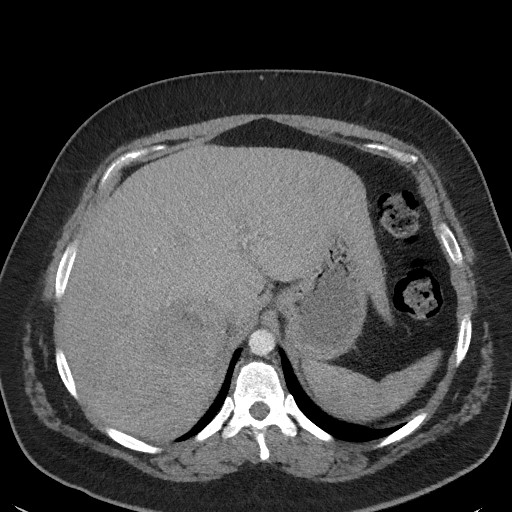
Contrast-enhanced abdominal CT, one axial slice; slice 41 of 56 in the series (ordered by position); reconstruction kernel I41f/3; 120 kVp; intravenous contrast given; soft-tissue window (W 400 / L 40 HU); 5 mm slice thickness; 512 × 512 image matrix, field of view 373 × 373 mm. Female patient, age 35 years. Case-level facts recorded for this patient, not image findings: diagnosis: adrenocortical carcinoma; tumour side: right adrenal; tumour size at pathology: 15 cm; Ki-67 index: 40 %; stage (as recorded): 2.
Annotated regions visible in this slice (semi-automatically segmented with operator editing):
- mass: bounding box (x1, y1, x2, y2) in pixels: (151, 304, 221, 363)